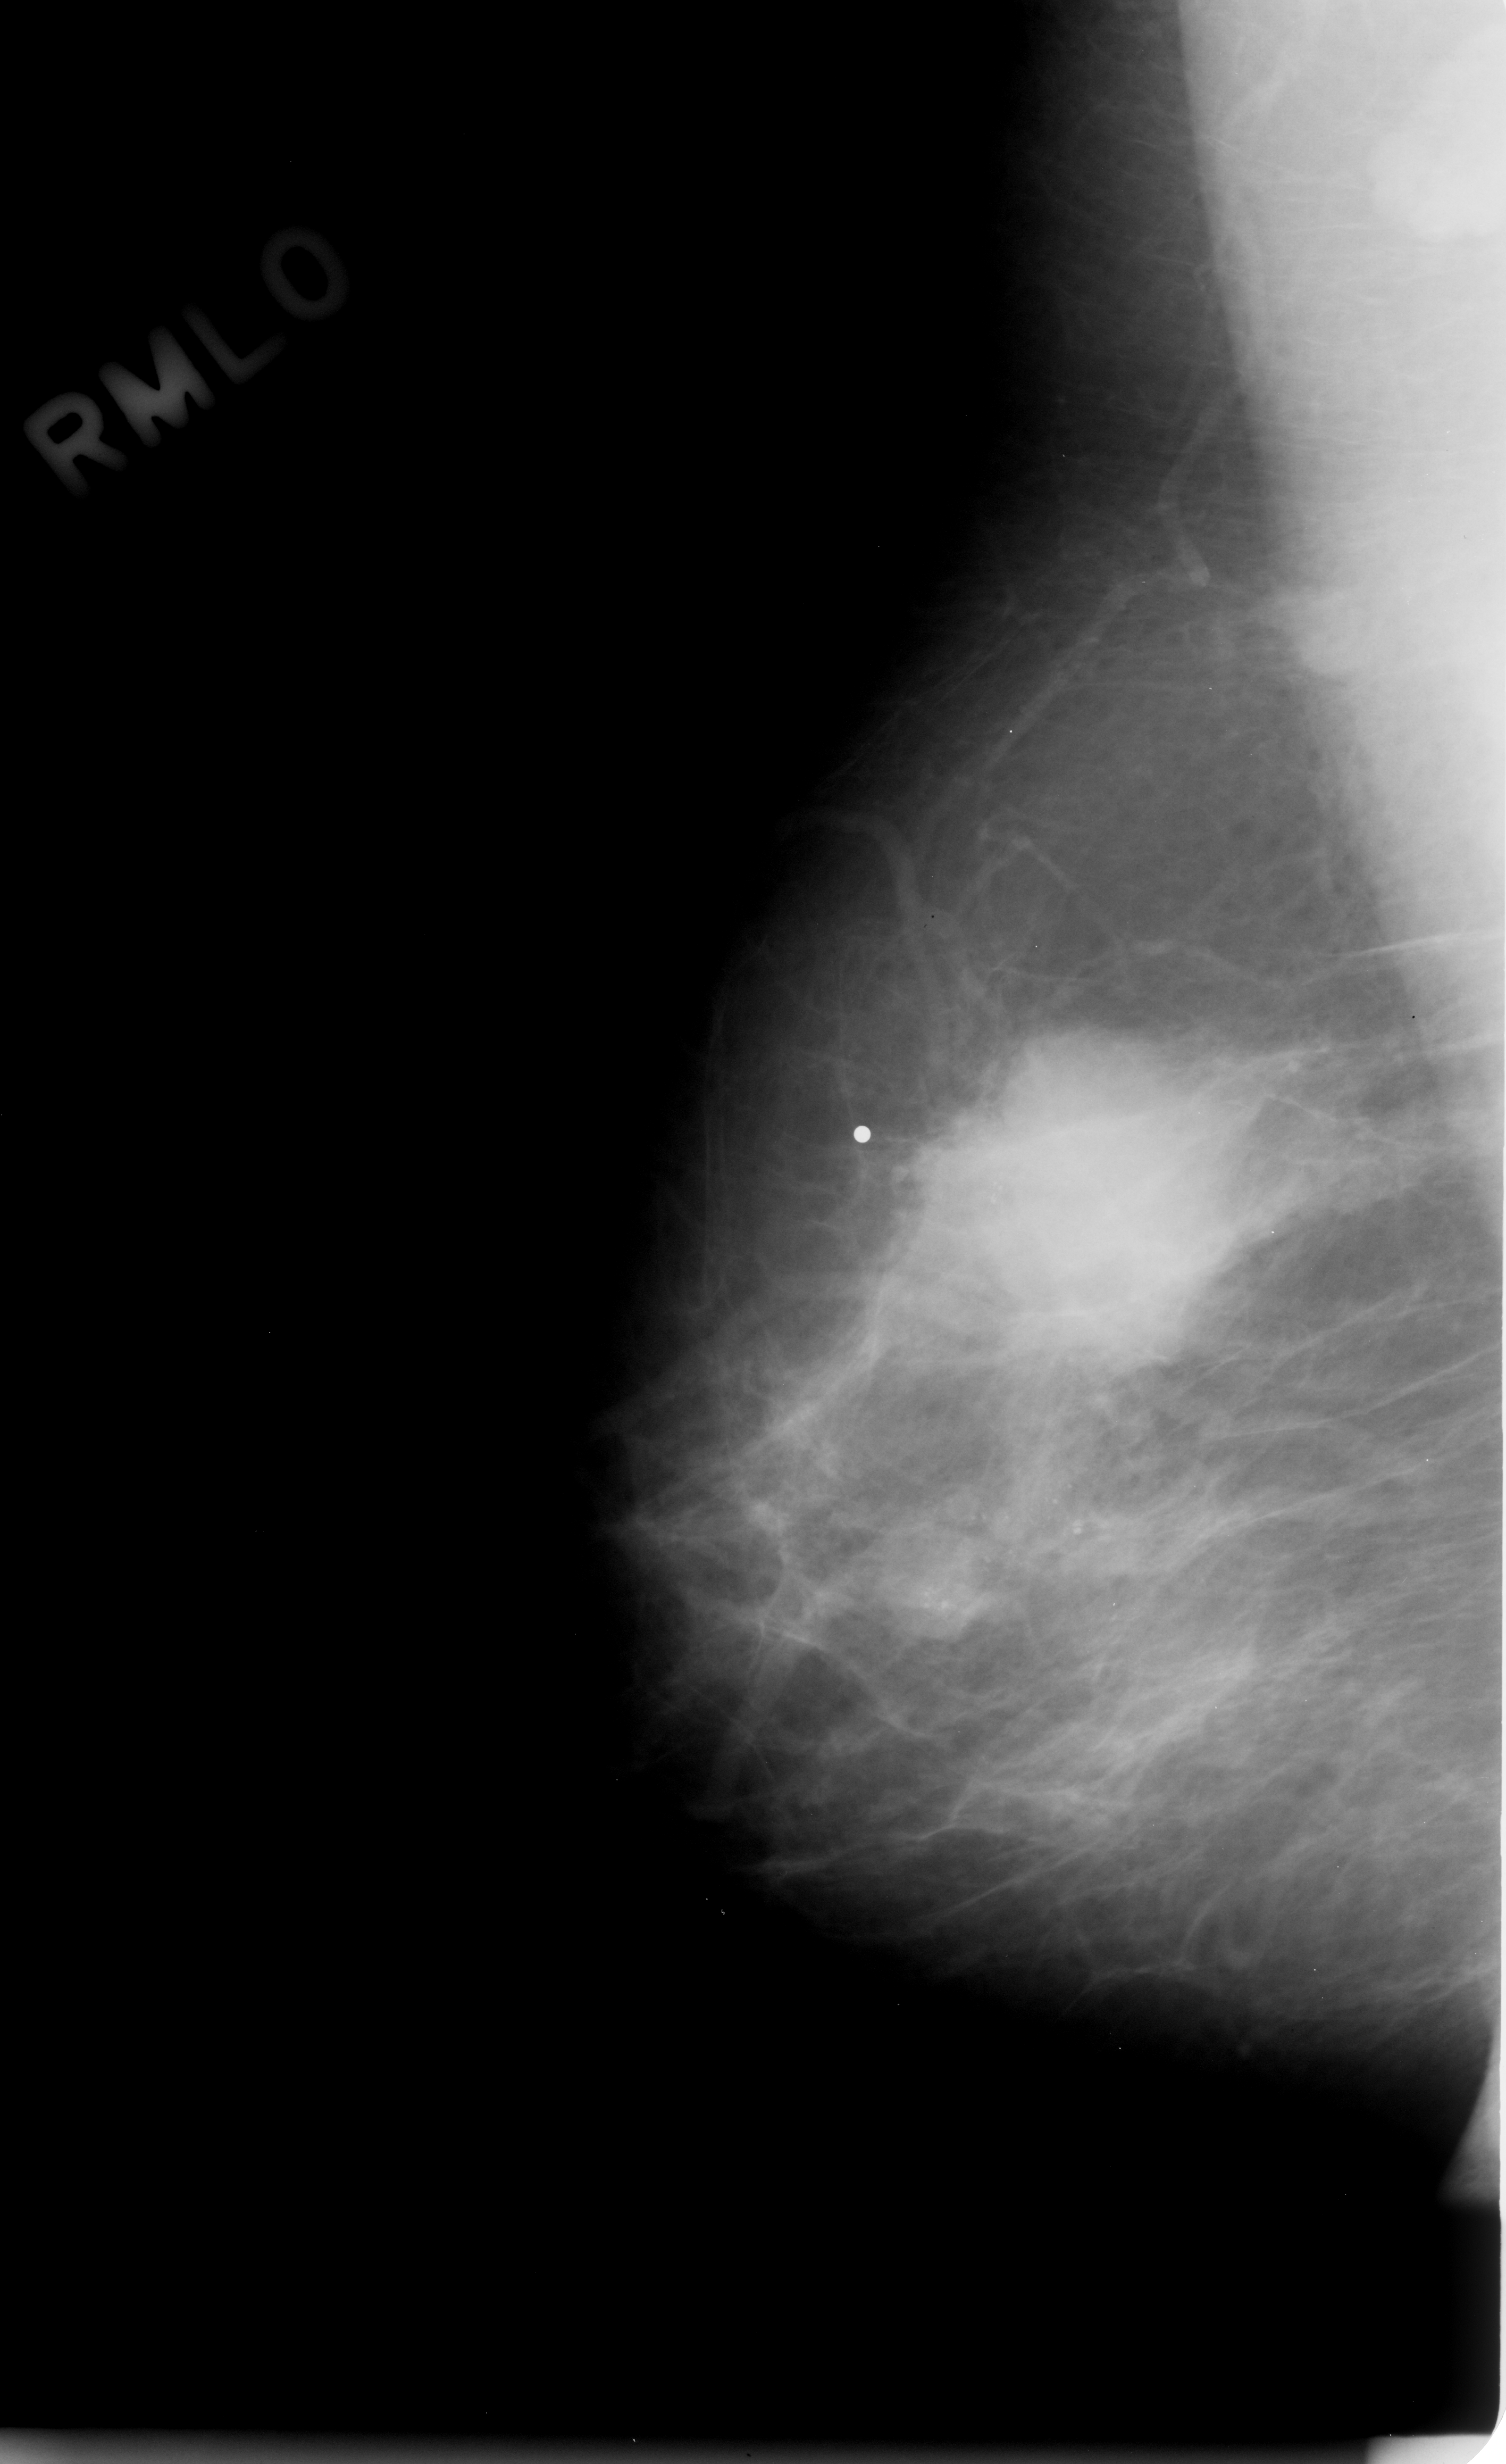
Mammogram (digitized film), right breast, MLO view, breast composition: almost entirely fatty (BI-RADS density category 1 of 4).
Radiologist-marked abnormalities on this image: Finding 1 of 2: mass, shape irregular, margins microlobulated; BI-RADS assessment category 5; subtlety rating 5 on a 1 (subtle) to 5 (obvious) scale; pathology (as recorded): malignant. Finding 2 of 2: mass, shape irregular, margins microlobulated; BI-RADS assessment category 5; subtlety rating 5 on a 1 (subtle) to 5 (obvious) scale; pathology result (as recorded, not read from the image): malignant.